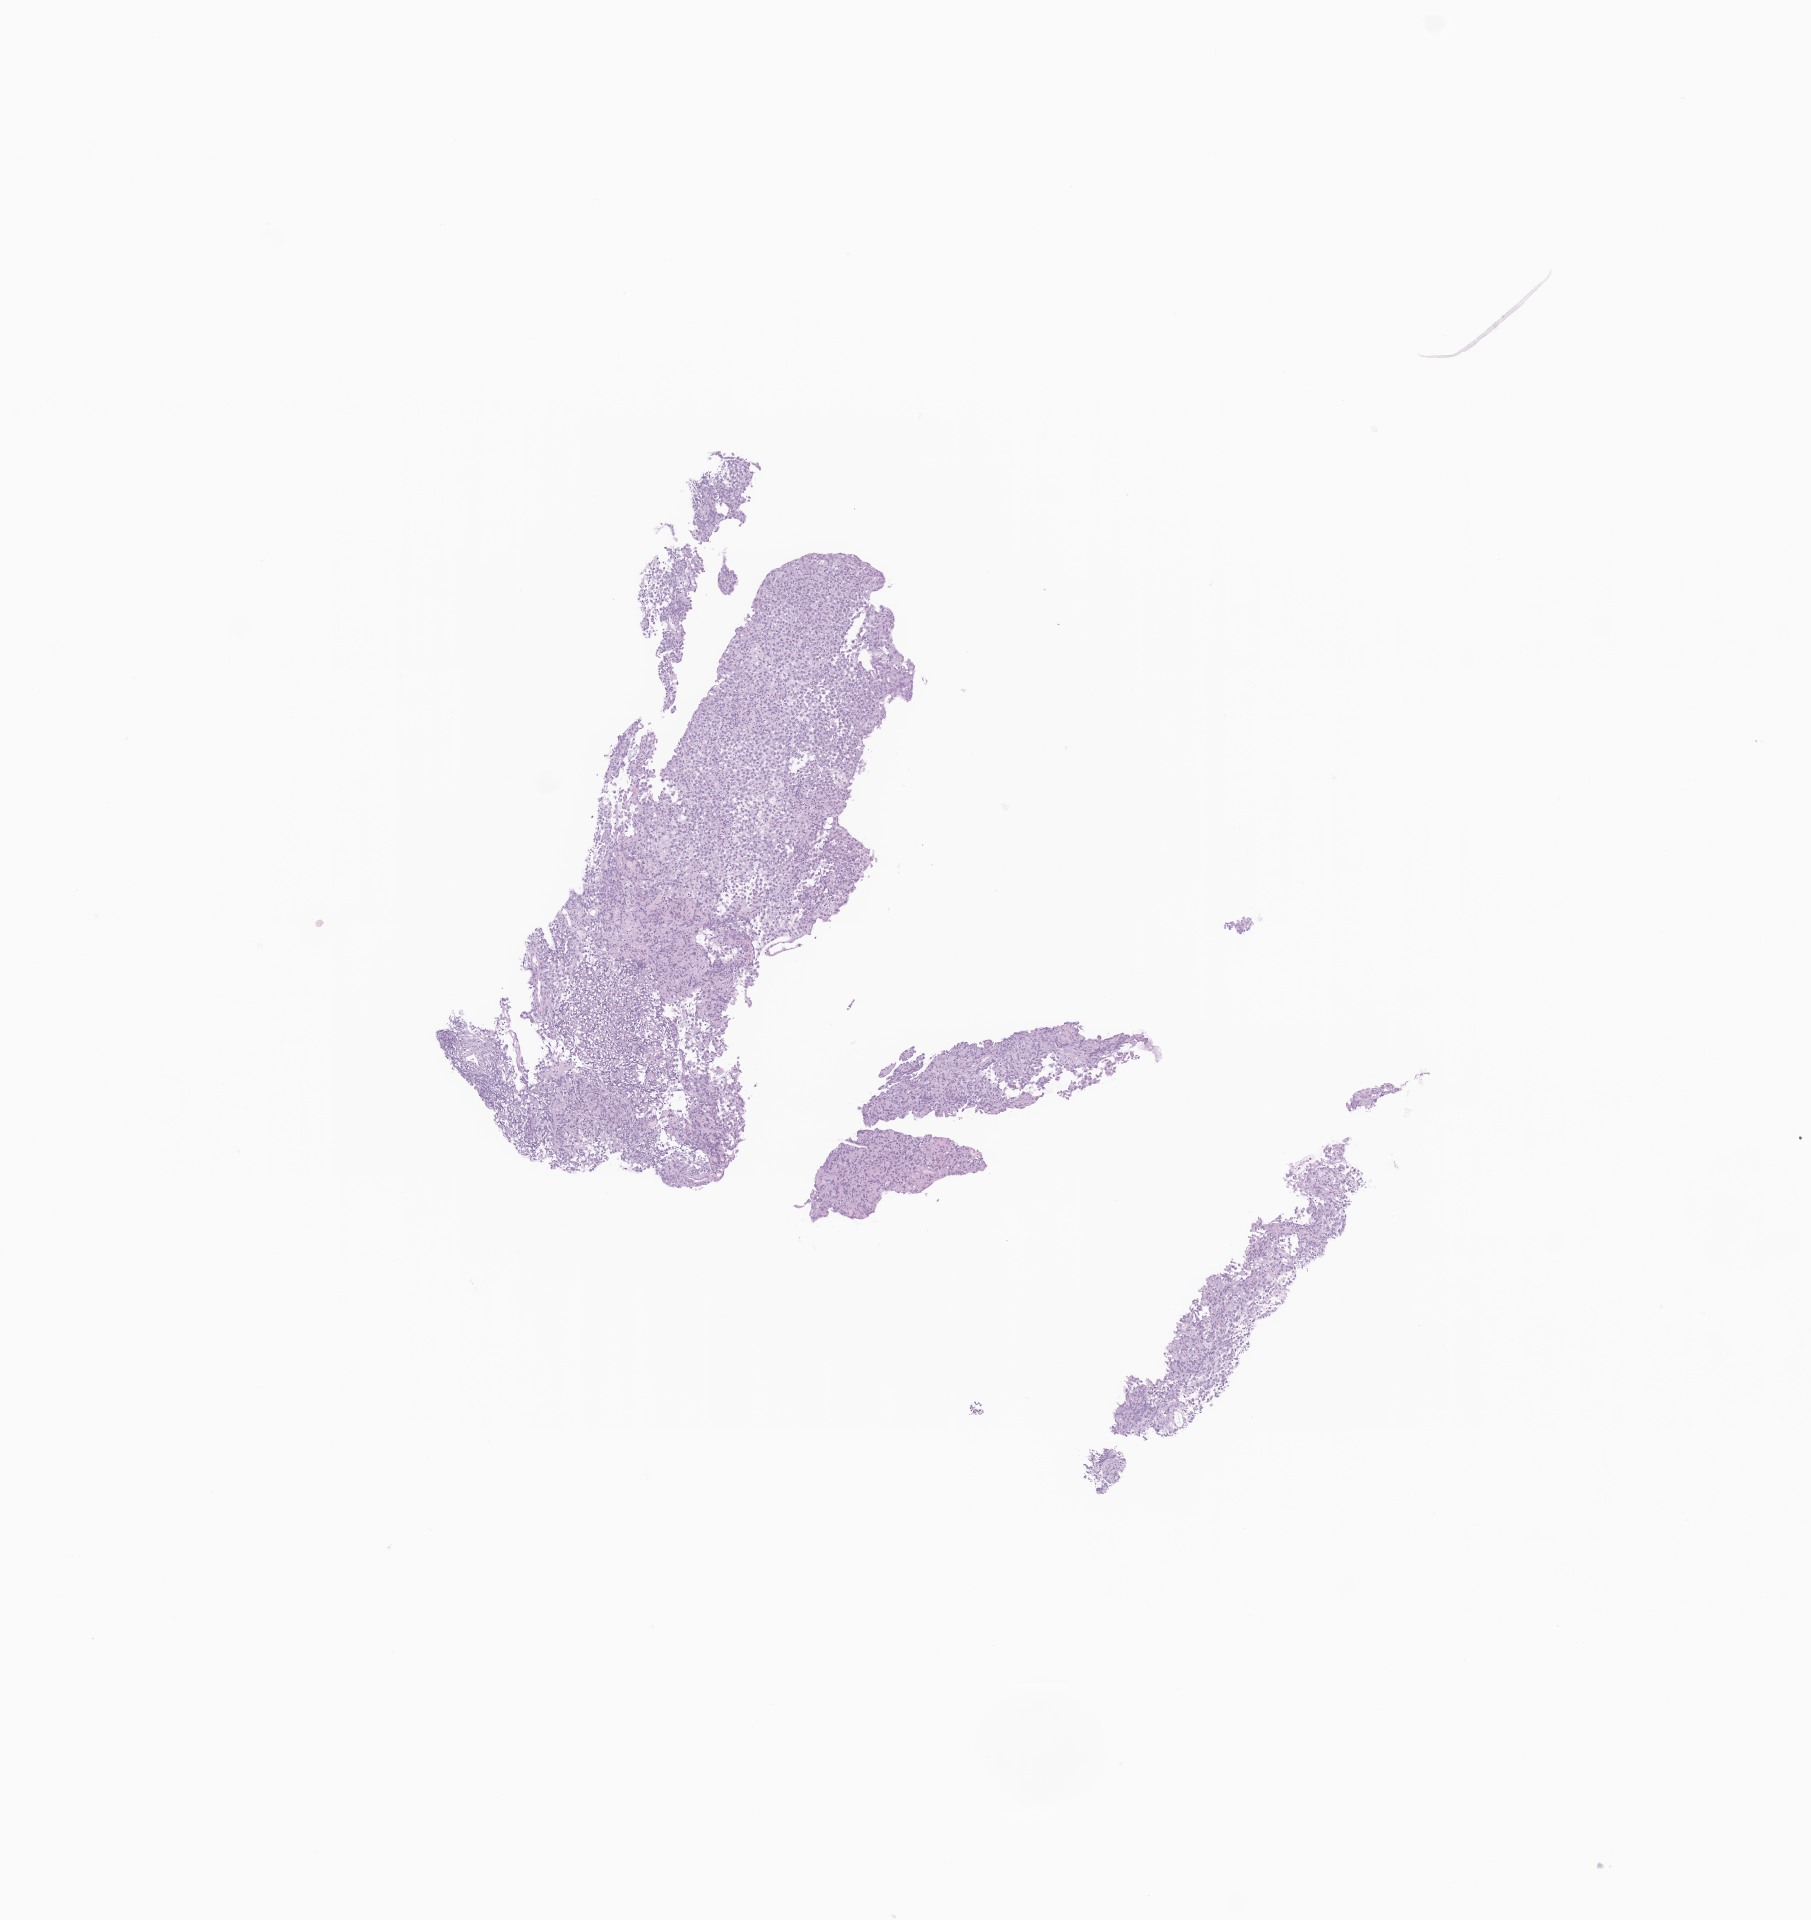
Digitized hematoxylin and eosin (H&E)-stained section of tumor tissue from the spinal cord, shown as a low-resolution overview of the whole scanned area (about 7.6 x 8.1 mm); FFPE section. Patient: female, age 144 months (12 years).
Diagnosis (ICD-O-3 morphology term): Ependymoma, NOS.